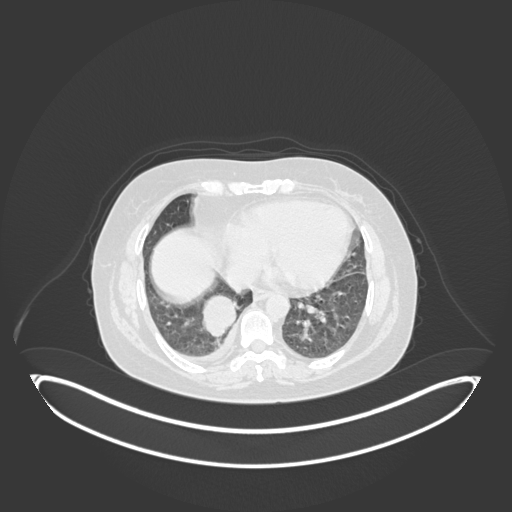
Chest CT, one axial slice. Position 47 of 231 along the scan axis. 120 kVp. Lung window (W 1500 / L -600 HU). 1 mm slice thickness. 512 × 512 image matrix, field of view 500 × 500 mm. Patient: female, 56 years. From the clinical record (not read from this slice): clinical TNM (as recorded): T2b N1 M0.
Outlined on this slice (rectangle marked by the reading radiologist):
- lung tumour (recorded histology: small cell carcinoma): box from (x=198, y=294) to (x=246, y=343) px